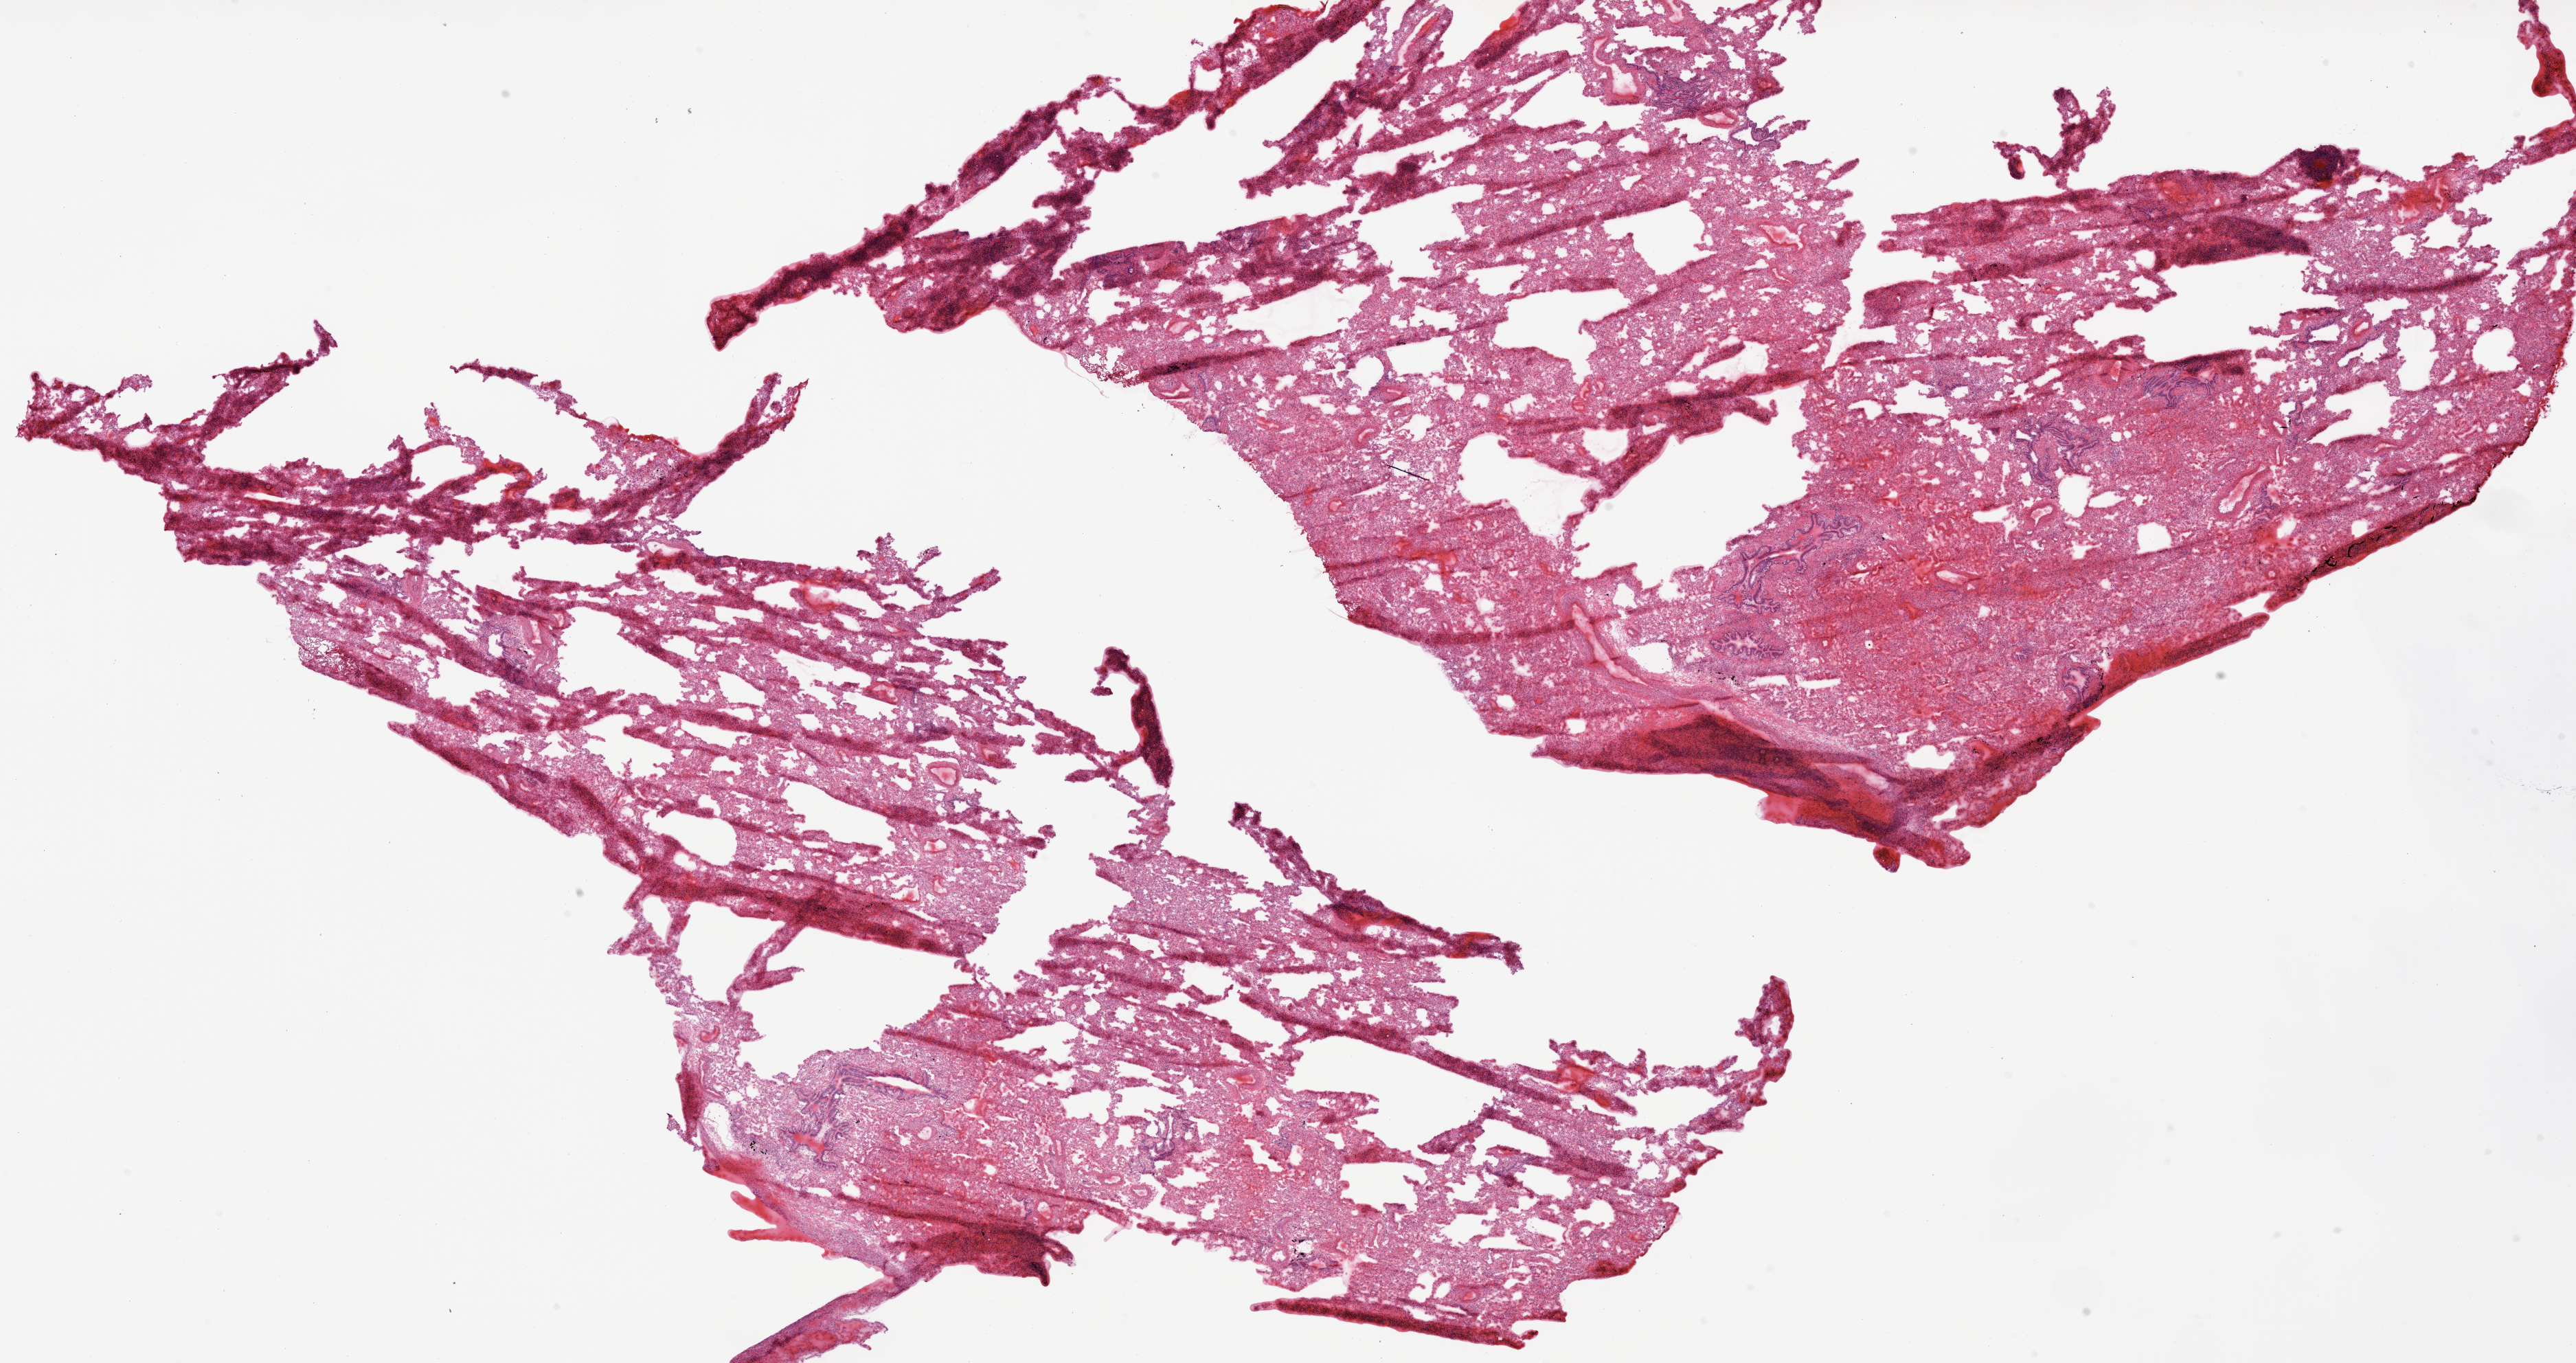
Whole-slide histology image, H&E — shown as a low-resolution overview of the whole scanned area (about 30.1 x 15.9 mm, acquisition: 20x scan). Frozen section from the bottom of the tissue portion. Solid tissue normal (non-tumour tissue) sample from the lung. Patient: male, age at initial diagnosis 66 years.
This section: solid tissue normal (non-tumour) sample from the same patient. Patient diagnosis: Adenocarcinoma, NOS.